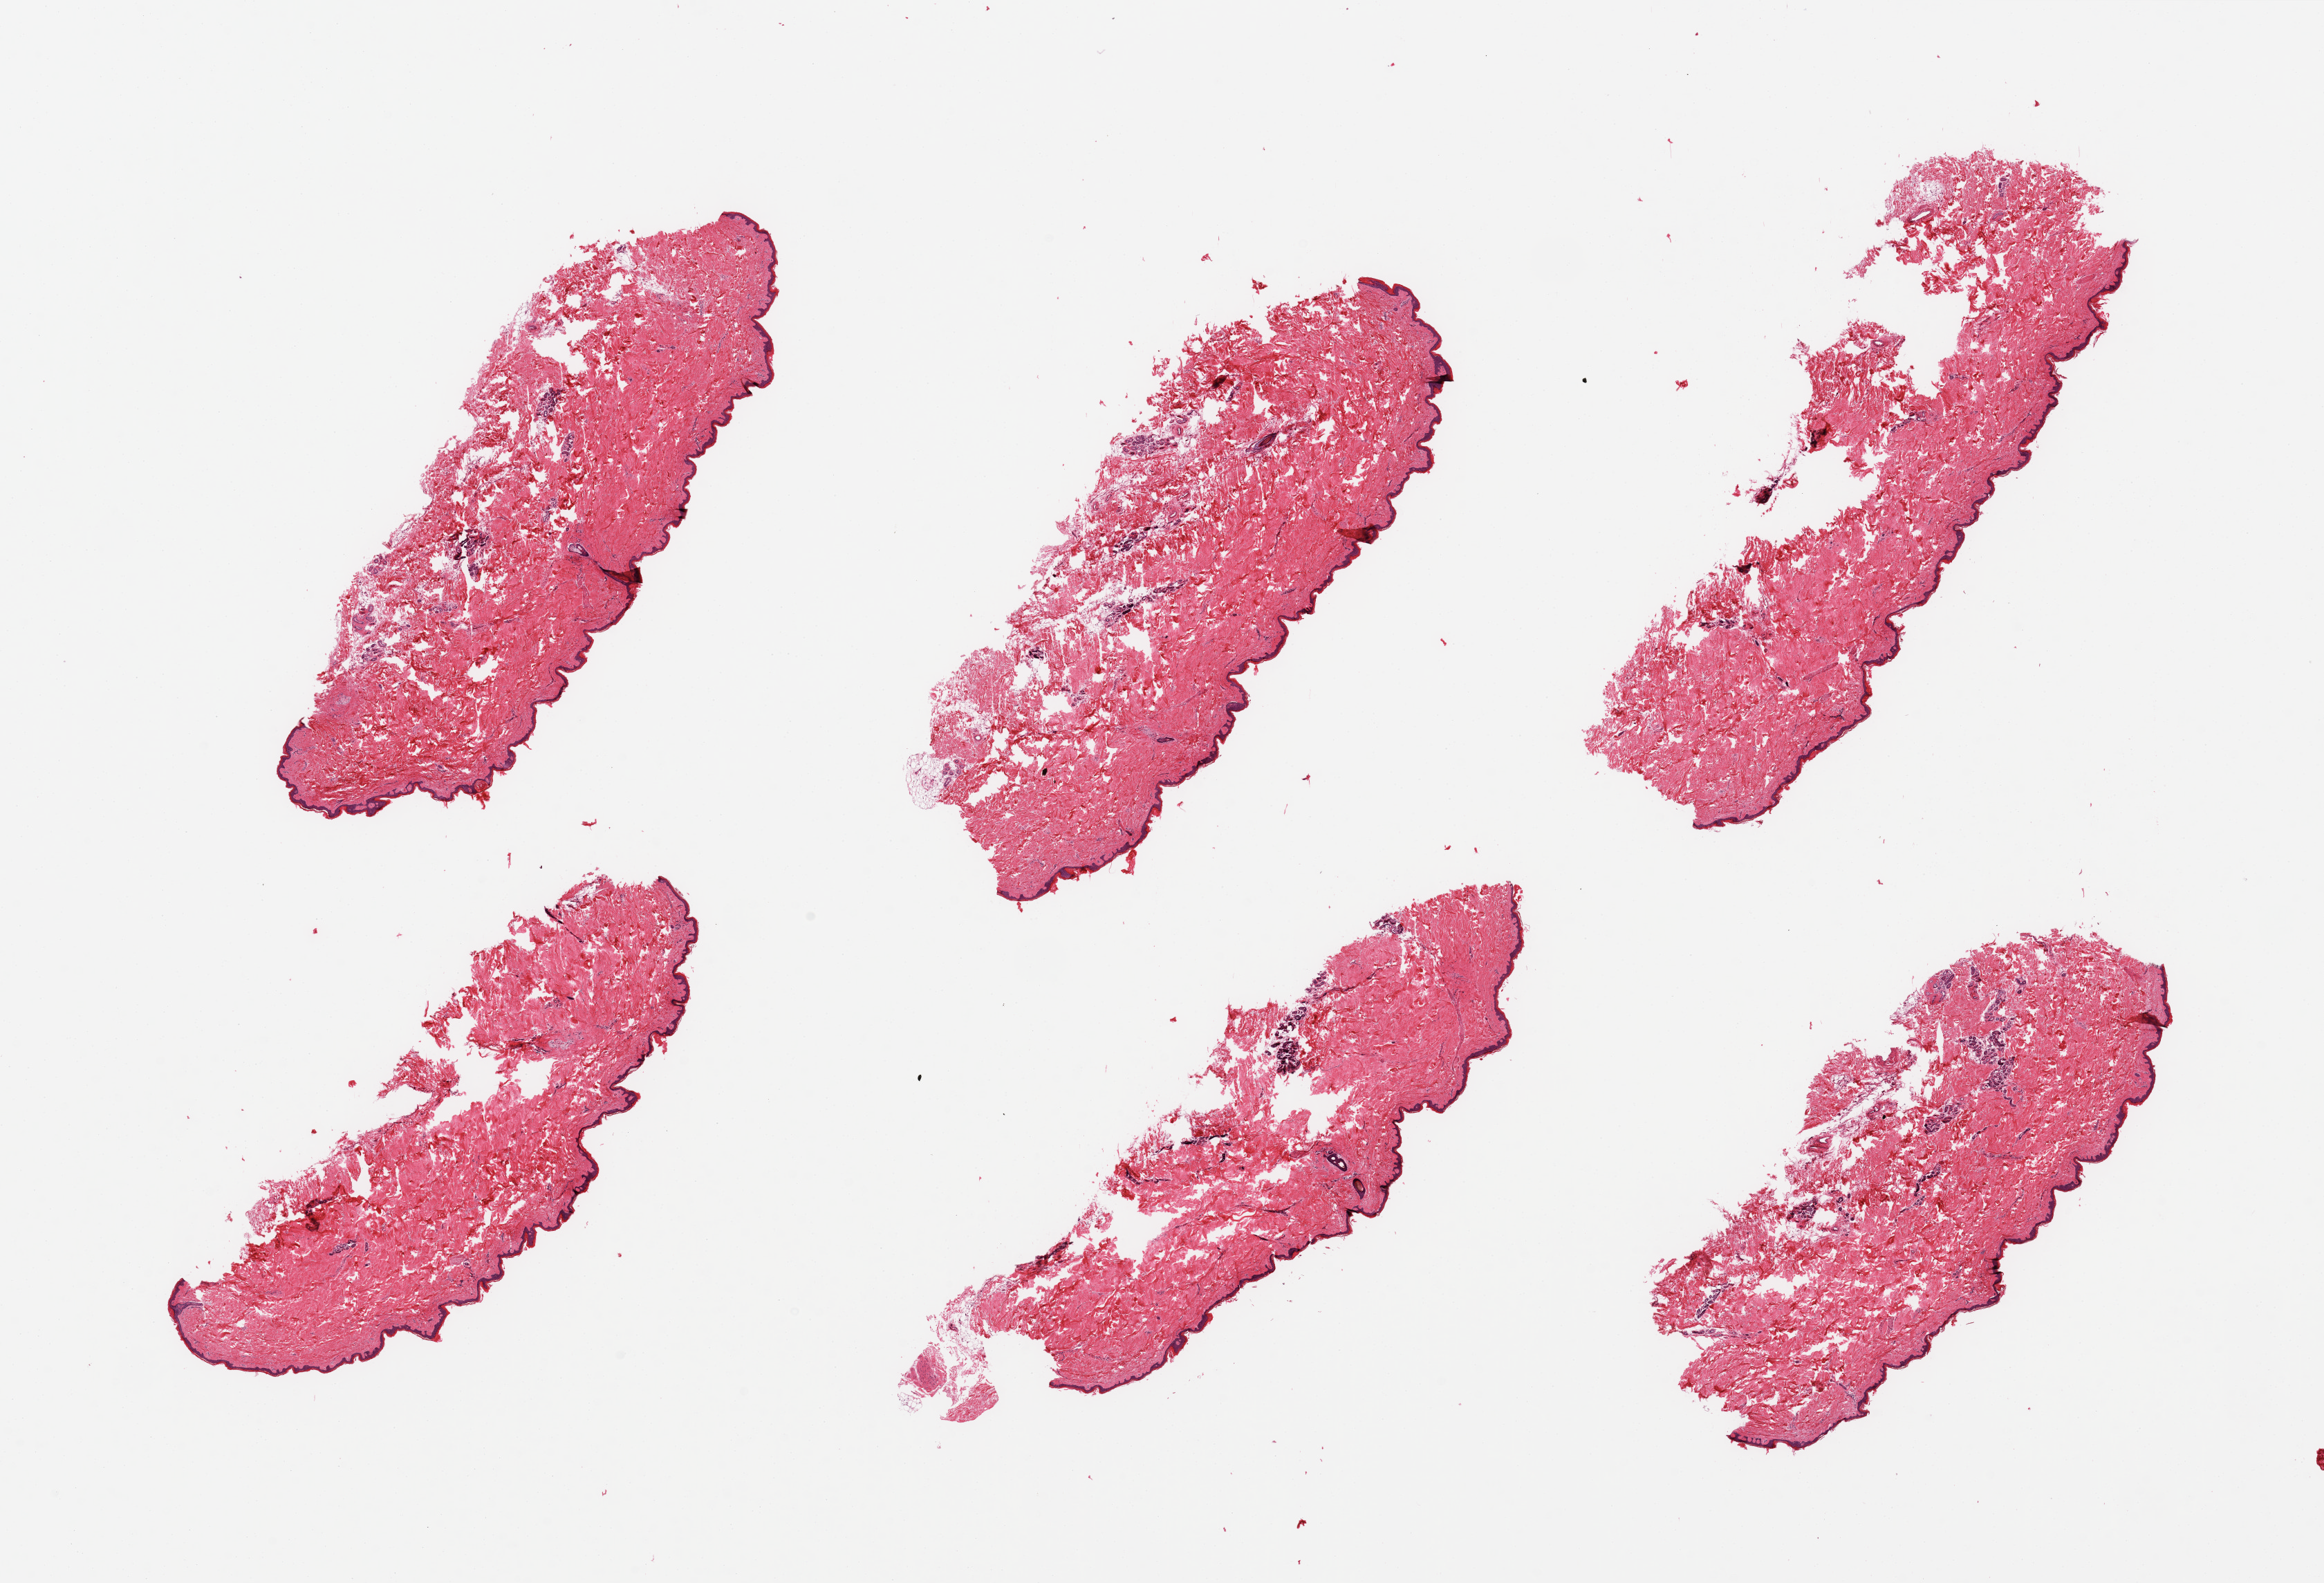
Haematoxylin and eosin whole-slide image, brightfield, shown as a low-resolution overview of the whole scanned area (about 26.6 x 18.1 mm, from a 20x scan); PAXgene-fixed, paraffin-embedded tissue; section of skin of lower leg (target tissue); tissue donor sample. Donor sex: male.
* review note (as recorded): 6 pieces, no significant dermal fat; squamous epithelium is ~35 microns